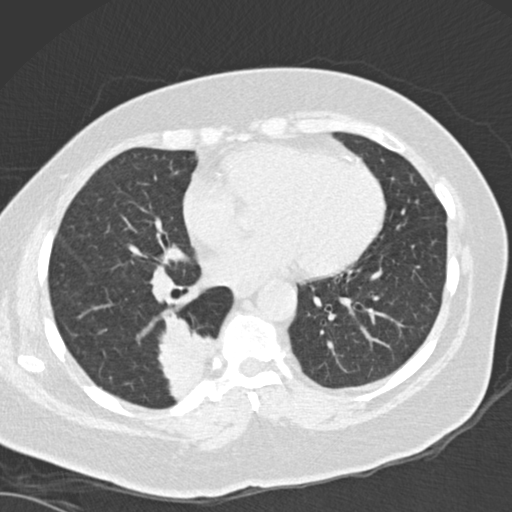
Low-dose screening chest CT, axial slice; baseline annual screen; lung window (W 1500 / L -600 HU); 2 mm slice thickness; slice 96 of 162 in the series. Female participant, aged 66 years at enrolment. Current smoker at enrolment.
Expert-annotated lung lesion, bounding box (x1, y1, x2, y2) in pixels: (150, 320, 227, 399). The screening reader recorded 3 non-calcified nodules or masses ≥4 mm on this exam (left lower lobe, left lower lobe, right lower lobe); which of them this box marks is not recorded. Official screen result: positive, change unspecified: nodule(s) >= 4 mm or enlarging nodule(s), mass(es), or other non-specific abnormalities suspicious for lung cancer.